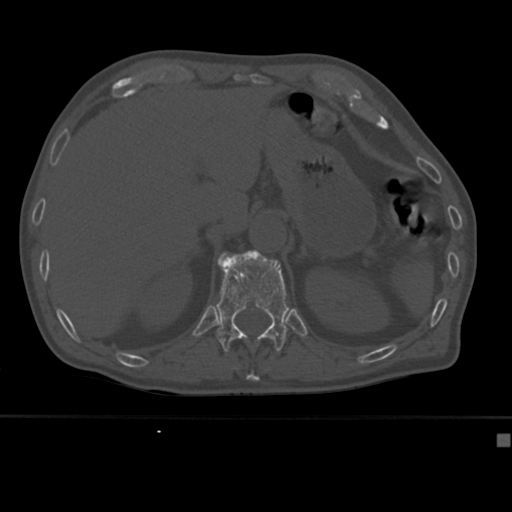
CT including the spine, one axial slice. Slice 193 of 430 in the series (ordered by position). Reconstruction kernel Br40s. 120 kVp. Bone window (W 1800 / L 400 HU). 1.5 mm slice thickness. 512 × 512 image matrix, field of view 337 × 337 mm. Male patient, age 64 years. From the clinical record (not read from this slice): primary cancer: uterus; vertebrae with lytic lesions (as recorded): T1, T4, T5, T7, L5.
Outlined on this slice (semi-automatically segmented with operator editing):
- L1 vertebra: bounding box (x1, y1, x2, y2) in pixels: (218, 256, 221, 259)
- T11 vertebra: (246, 372, 260, 382)
- T12 vertebra: (216, 250, 289, 353)